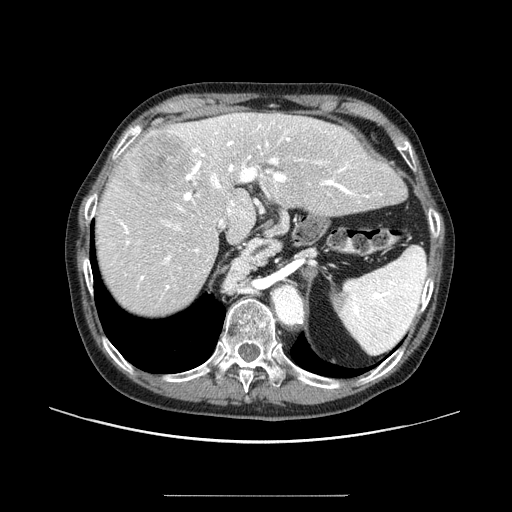
Contrast-enhanced abdominal CT (liver protocol), one axial slice; reconstruction kernel STANDARD; 100 kVp; one of 2 acquisitions stored at this slice position; soft-tissue window (W 400 / L 40 HU); 2.5 mm slice thickness; 512 × 512 image matrix, field of view 400 × 400 mm. Case-level facts recorded for this patient, not image findings: diagnosis: hepatocellular carcinoma (patient treated with transarterial chemoembolisation; whether this scan precedes or follows treatment is not stated here); TNM stage (as recorded): Stage-I; Child-Pugh class: A; tumour differentiation: moderately differentiated.
Outlined on this slice (semi-automatic segmentation, software-assisted and operator-edited):
- liver parenchyma outside the tumour (the mass and vessels are separate outlines, so this box may not span the whole liver): bounding box [x1, y1, x2, y2] px = [96, 112, 397, 314]
- mass: [130, 129, 191, 187]
- liver vessels: [106, 114, 350, 290]